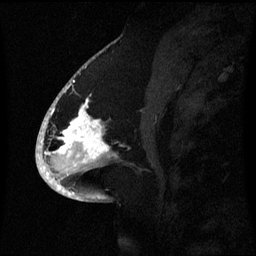
Breast MRI (dynamic contrast-enhanced), one sagittal slice. Position 32 of 60 along the scan axis. Dynamic contrast-enhanced series, image 2 of 3 at this slice position (ordered by acquisition). 1.5 T. TE 4.2 ms, TR 8.4 ms. 256 × 256 image matrix. Female patient, age 53 years. Case-level facts recorded for this patient, not image findings: setting: breast cancer imaged before/during neoadjuvant chemotherapy; receptor status: HR-positive, HER2-negative.
Structures marked on this image (semi-automatically segmented with operator editing):
- analysis volume of interest (the breast-tissue region the enhancement analysis was run in; not a lesion): bounding box [x1, y1, x2, y2] px = [52, 90, 120, 171]
- tumour enhancement mask (voxels above the 70 % enhancement threshold inside the analysis volume of interest): [52, 90, 110, 161]